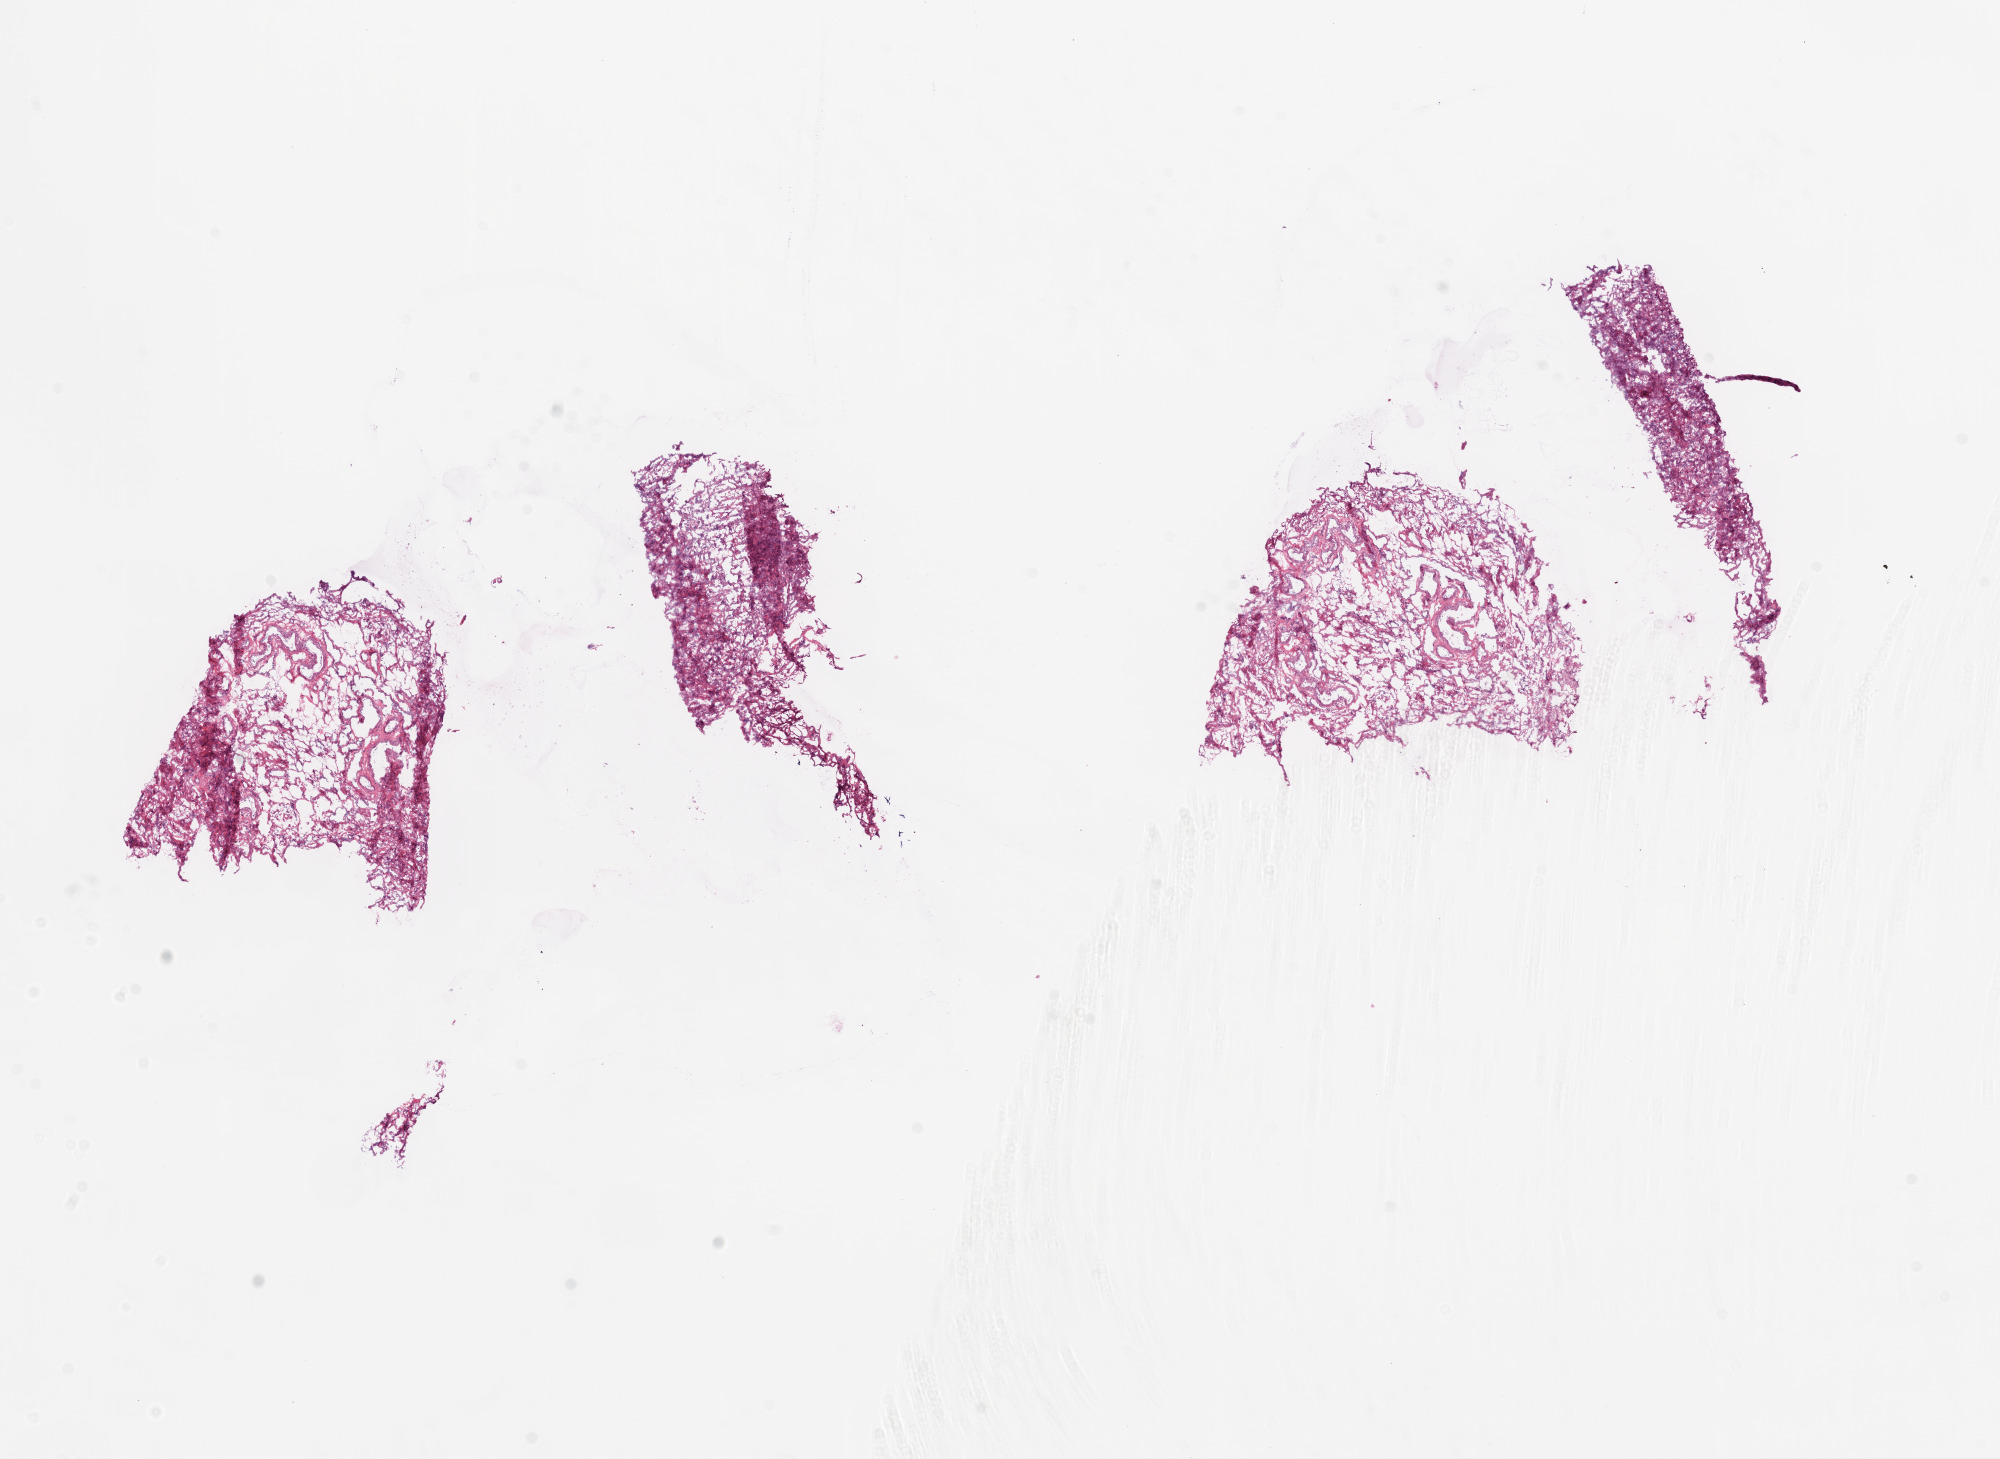
Hematoxylin and eosin (H&E) stained whole-slide image — a low-resolution overview of the entire scanned area, about 16.0 x 11.7 mm, frozen section, ovary, solid tissue normal (non-tumour tissue) sample. Female patient; age at initial diagnosis 44 years.
- this section: solid tissue normal (non-tumour) sample from the same patient
- patient diagnosis: Serous cystadenocarcinoma, NOS